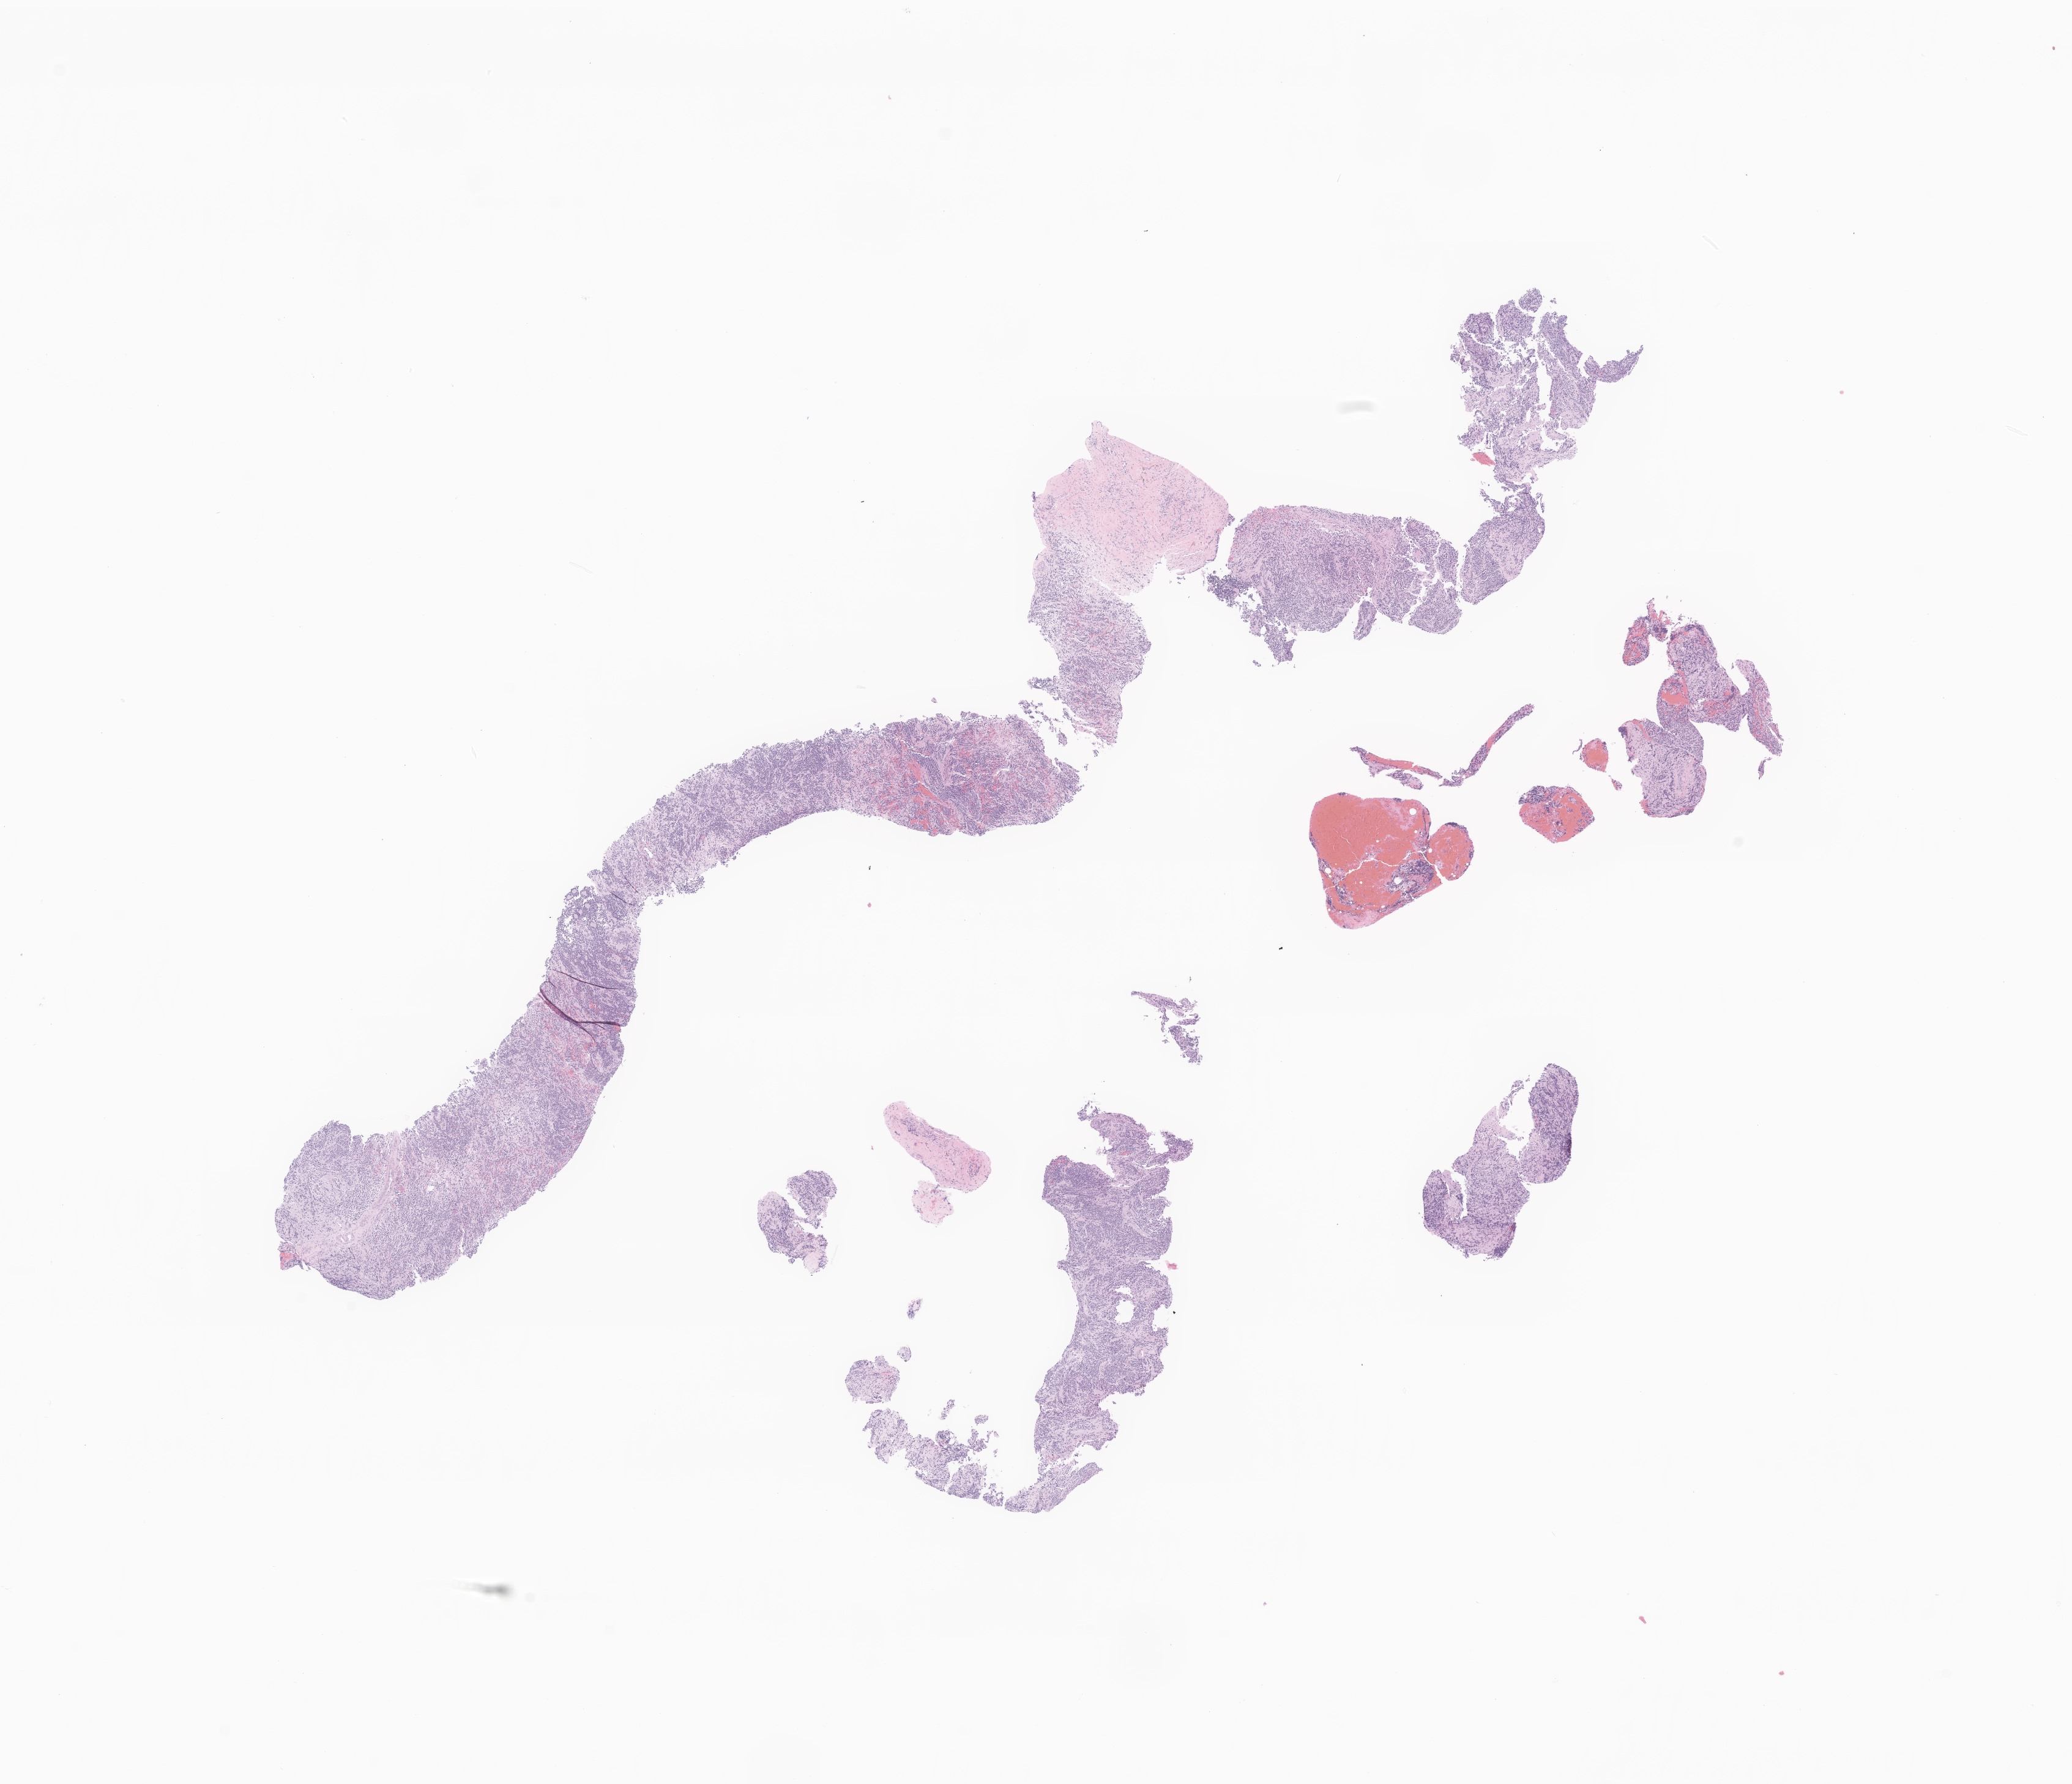
Haematoxylin and eosin whole-slide image of tumor tissue from the spinal cord, a low-resolution overview of the entire scanned area, about 14.3 x 12.3 mm, FFPE section. Patient: male, age 113 days.
Recorded diagnosis: Neuroblastoma, NOS.